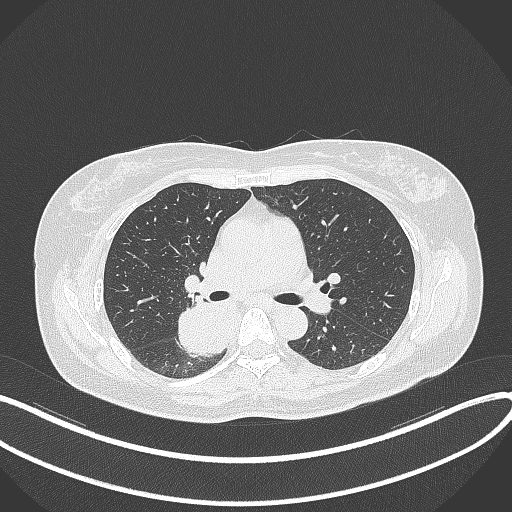
Chest CT, one axial slice; reconstruction kernel B70f; 120 kVp; lung window (W 1500 / L -600 HU); 1 mm slice thickness; 512 × 512 image matrix, field of view 400 × 400 mm. Female patient, age 54 years. Case-level facts recorded for this patient, not image findings: clinical TNM (as recorded): T4 N0 M0.
Structures marked on this image (rectangle marked by the reading radiologist):
- lung tumour (recorded histology: adenocarcinoma): bounding box [x1, y1, x2, y2] px = [173, 298, 229, 357]